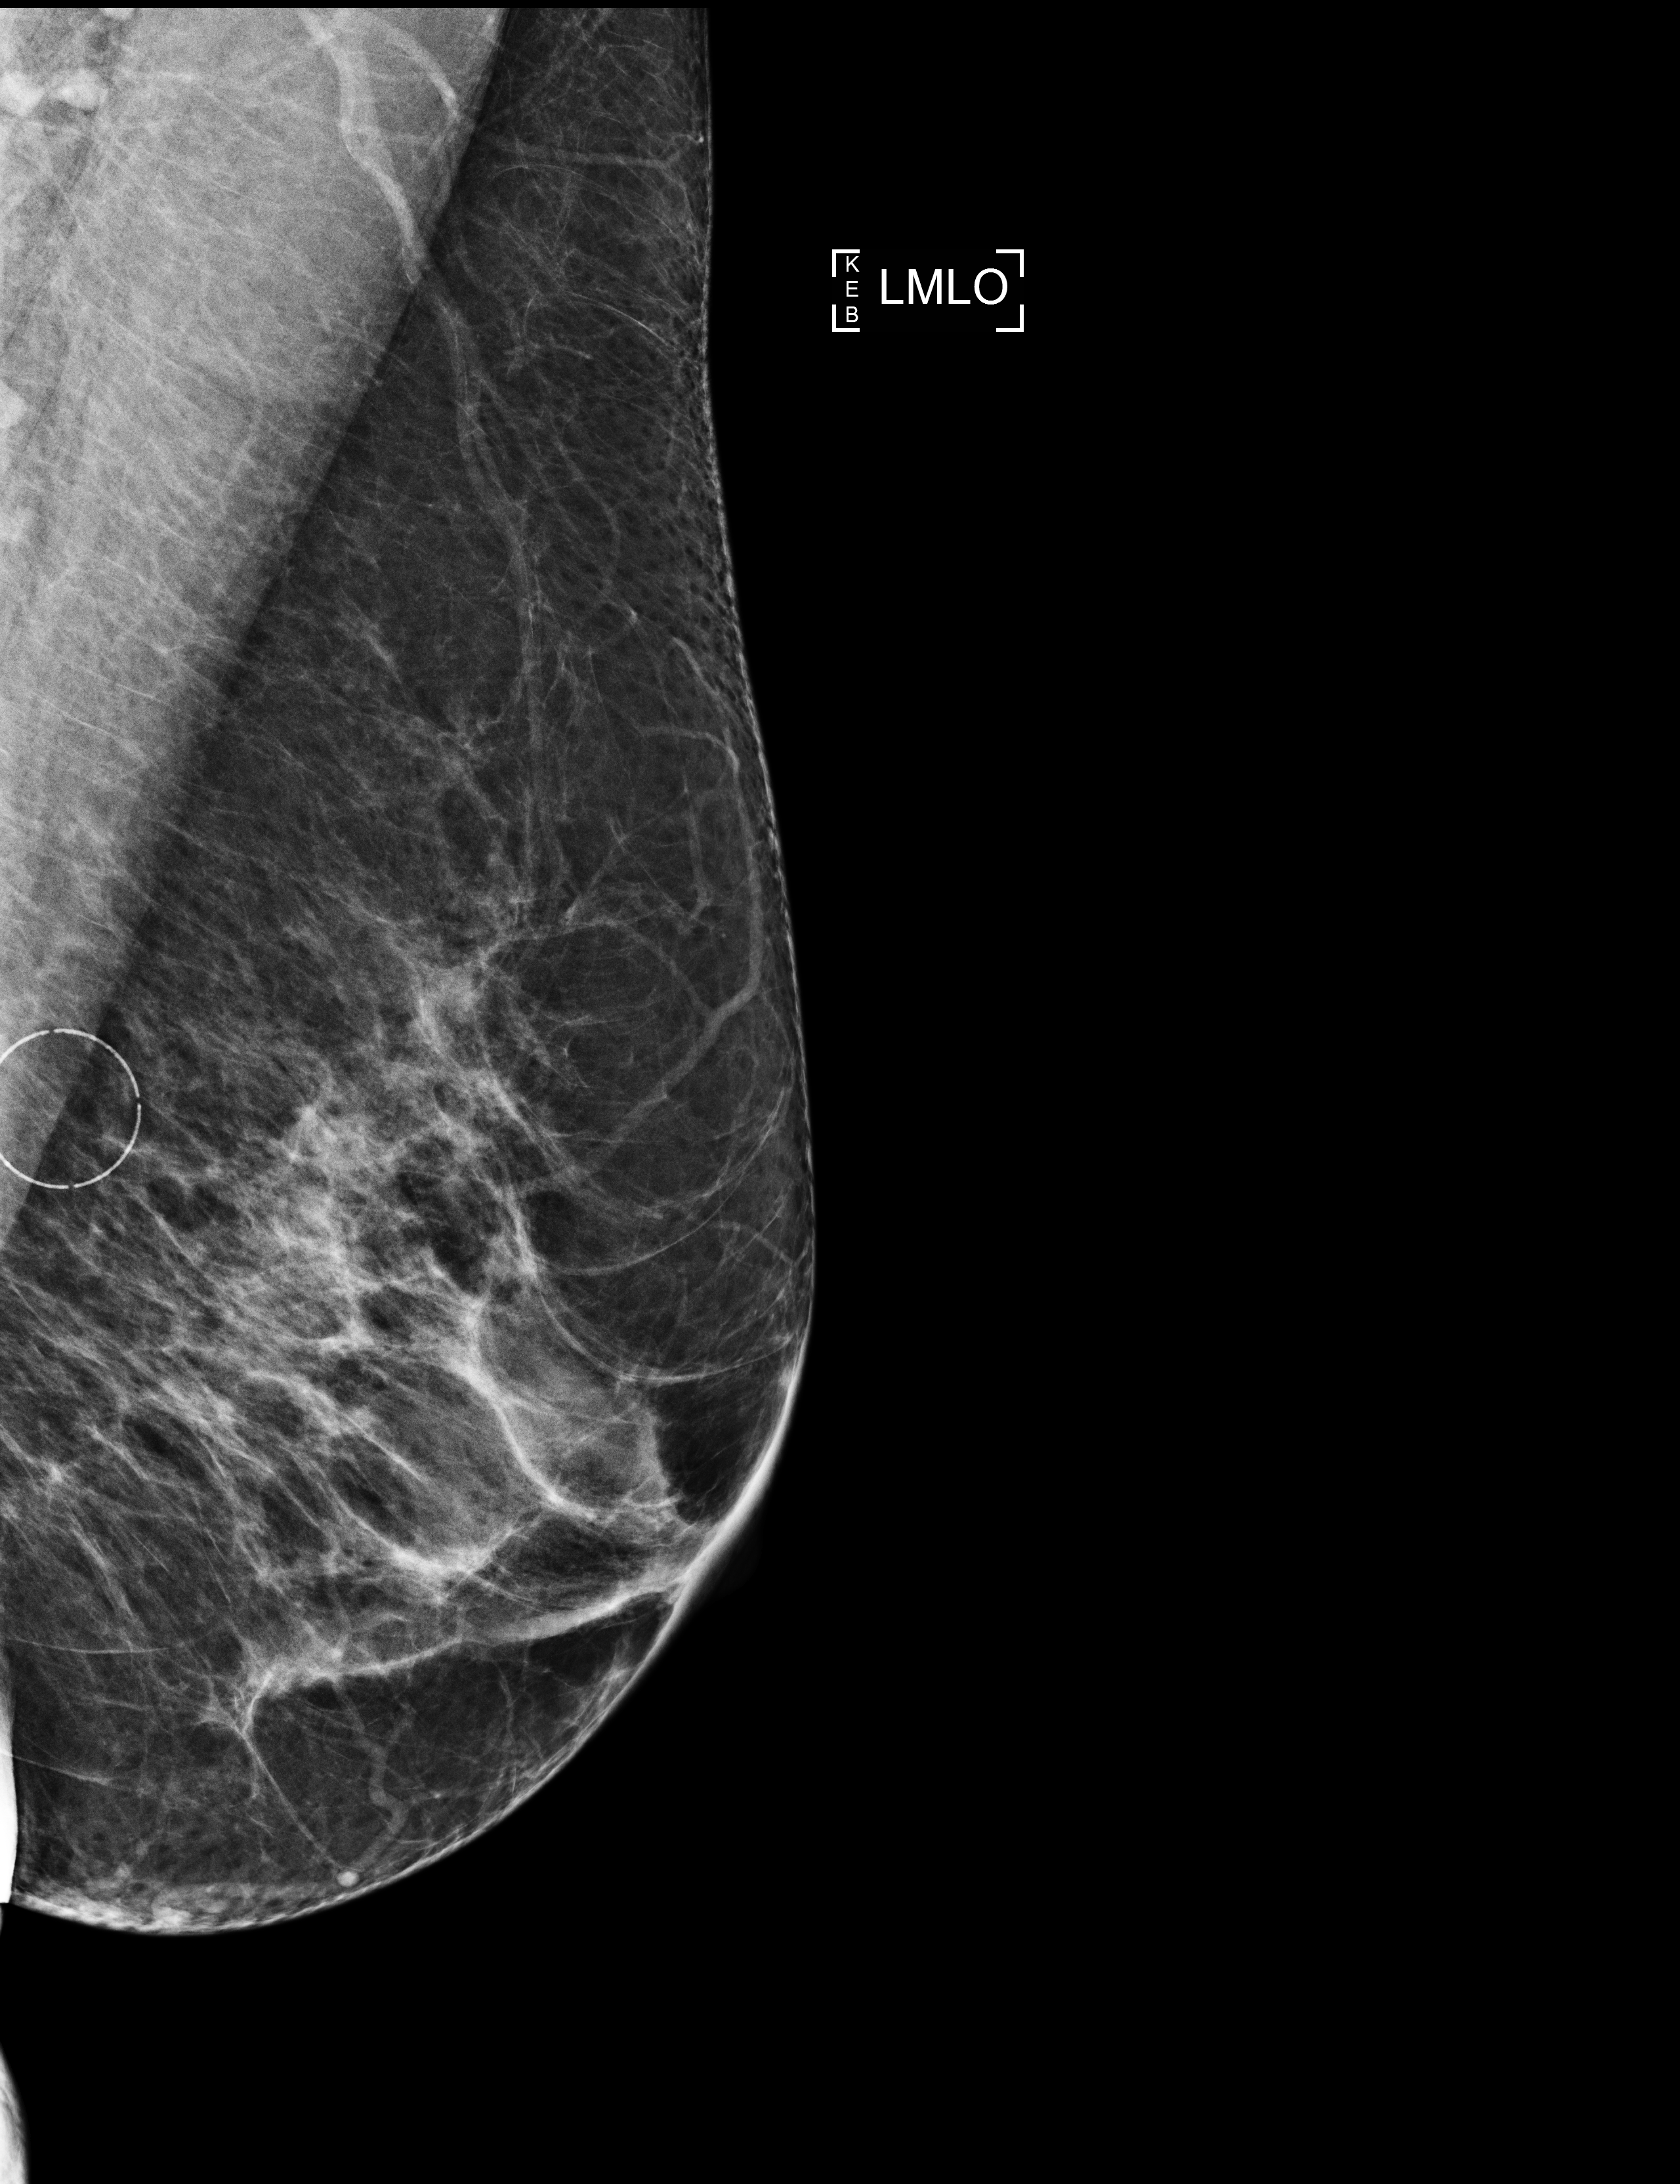
Annual screening mammography examination; compressed breast thickness 60 mm; system: Selenia Dimensions. Patient: female, 60 years.
Image type: full-field digital mammogram. Breast: left. Projection: mediolateral oblique (MLO) view. BI-RADS breast density category at the screening exam (both breasts, scale 1–4): 3. Final BI-RADS category for the screening round (tomosynthesis exam, both breasts): category 1. Recall: no recall after this screen.